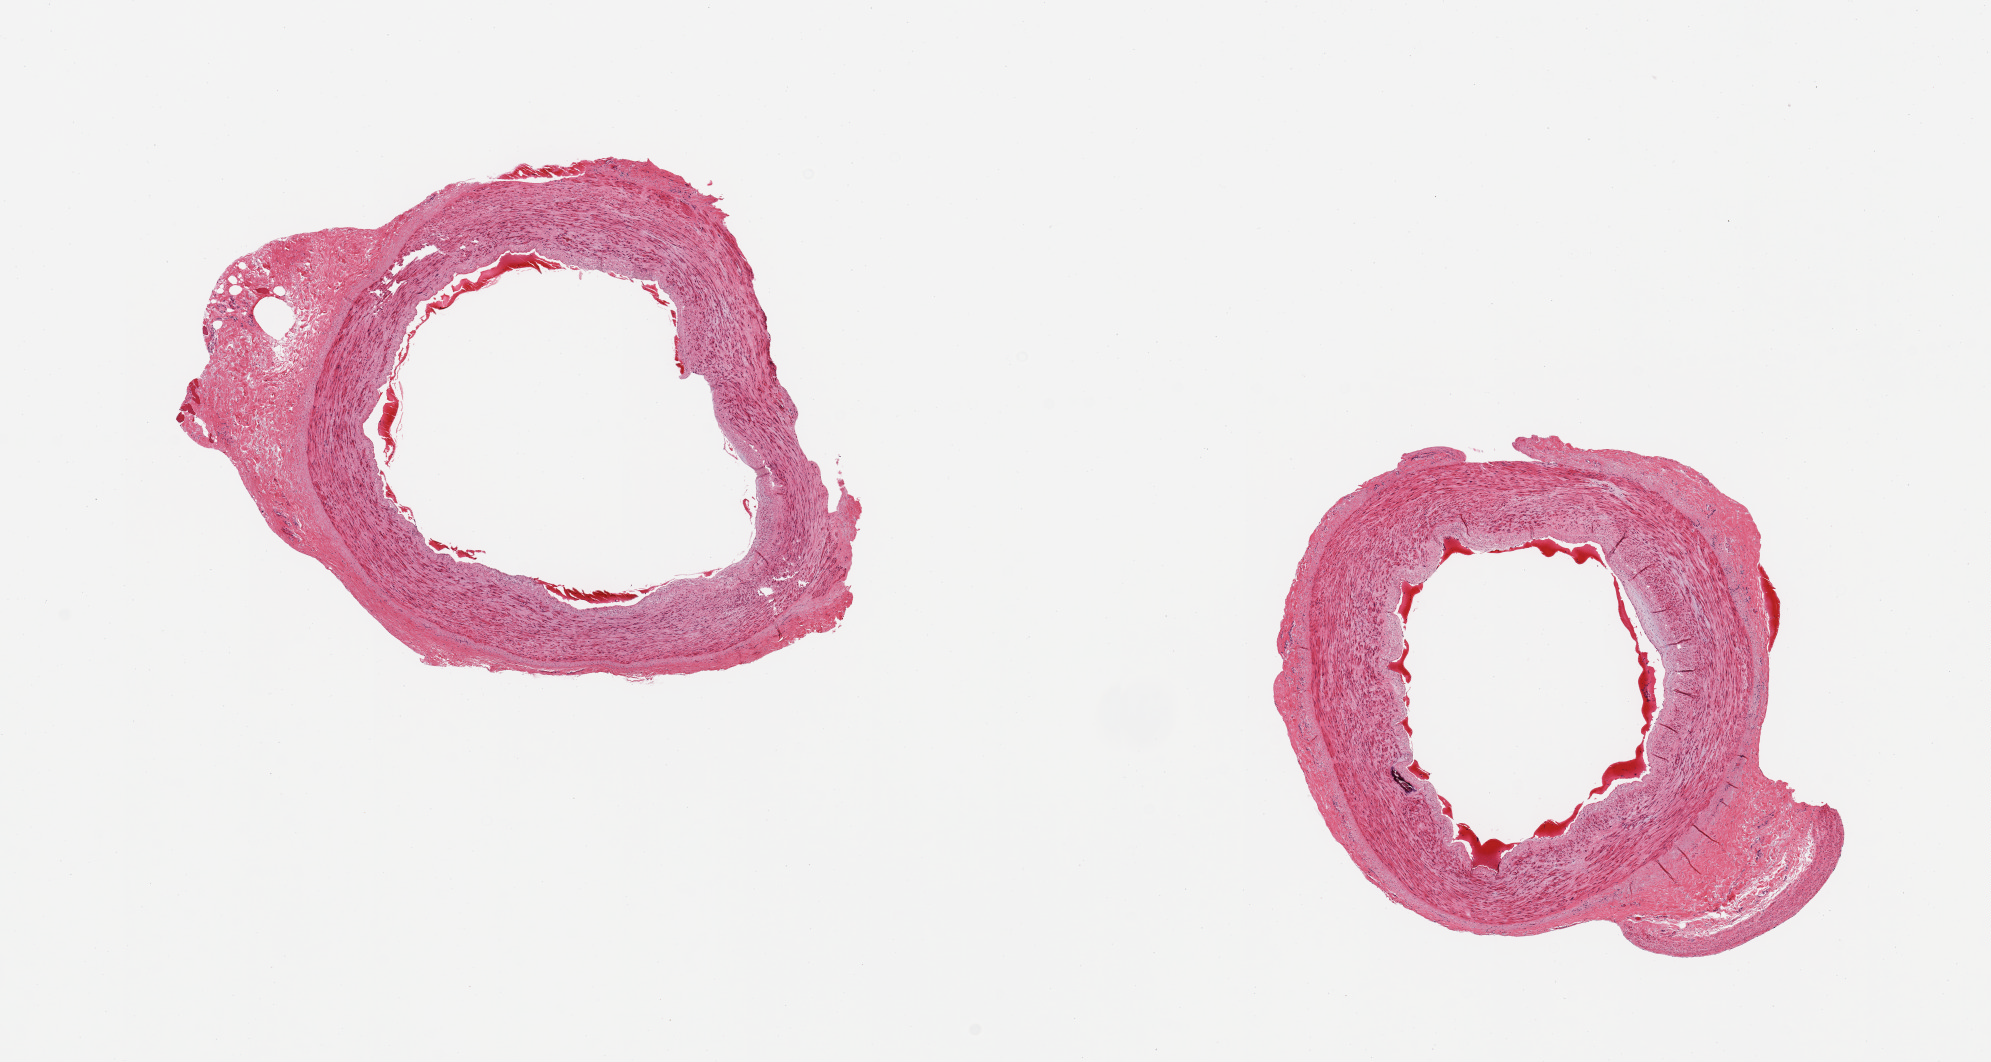
Whole-slide image, hematoxylin and eosin (H&E) stain — whole scanned area (about 15.8 x 8.4 mm) shown as a low-resolution overview, PAXgene-fixed, paraffin-embedded tissue, sampled site (target tissue): tibial artery, donor tissue sample. Donor sex: female.
Review note (as recorded): 2 pieces, clean sections, minimal atherosis.